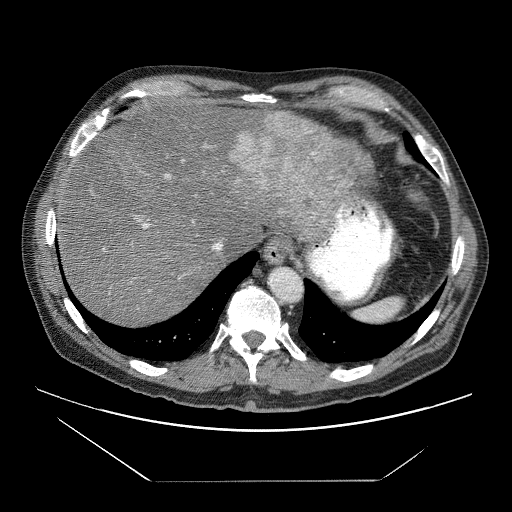
Contrast-enhanced abdominal CT (liver protocol), one axial slice. Position 57 of 83 along the scan axis. Soft-tissue window (W 400 / L 40 HU). 2.5 mm slice thickness. 512 × 512 image matrix, field of view 420 × 420 mm. From the clinical record (not read from this slice): diagnosis: hepatocellular carcinoma (patient treated with transarterial chemoembolisation; whether this scan precedes or follows treatment is not stated here); TNM stage (as recorded): Stage-IVB; Child-Pugh class: B.
Outlined on this slice (semi-automatically segmented with operator editing):
- liver parenchyma outside the tumour (the mass and vessels are separate outlines, so this box may not span the whole liver): bounding box [x1, y1, x2, y2] px = [56, 84, 372, 325]
- mass: [229, 111, 369, 235]
- liver vessels: [103, 85, 343, 294]